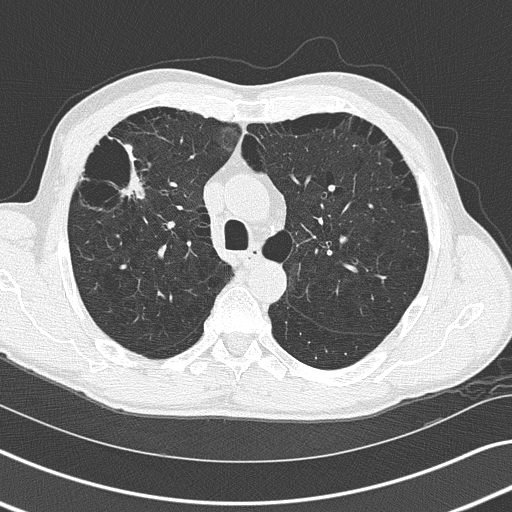
Low-dose screening chest CT, axial slice. Third annual screen. Lung window (W 1500 / L -600 HU). Lung (sharp) reconstruction kernel (B50f). Slice 57 of 170 in the series. 512 × 512 image matrix. Male participant, aged 66 years at enrolment. Current smoker at enrolment.
Expert-annotated lung lesion, box from (x=86, y=131) to (x=164, y=221) px. Screening reader's record for this exam (one nodule recorded; not confirmed to be the boxed lesion): non-calcified nodule or mass ≥4 mm, left lower lobe, 9 × 8 mm, smooth margins, soft tissue attenuation, pre-existing on the prior screen: yes; interval growth: no. Note: the box lies in the patient's right hemithorax on this image, whereas the reader's record names the left lung; they may be different findings. Participant outcome: lung cancer diagnosed 285 days after this screen — squamous cell carcinoma, adenoid, right upper lobe, poorly differentiated (G3), stage IIB (AJCC 6th edition), 50 mm at pathology.